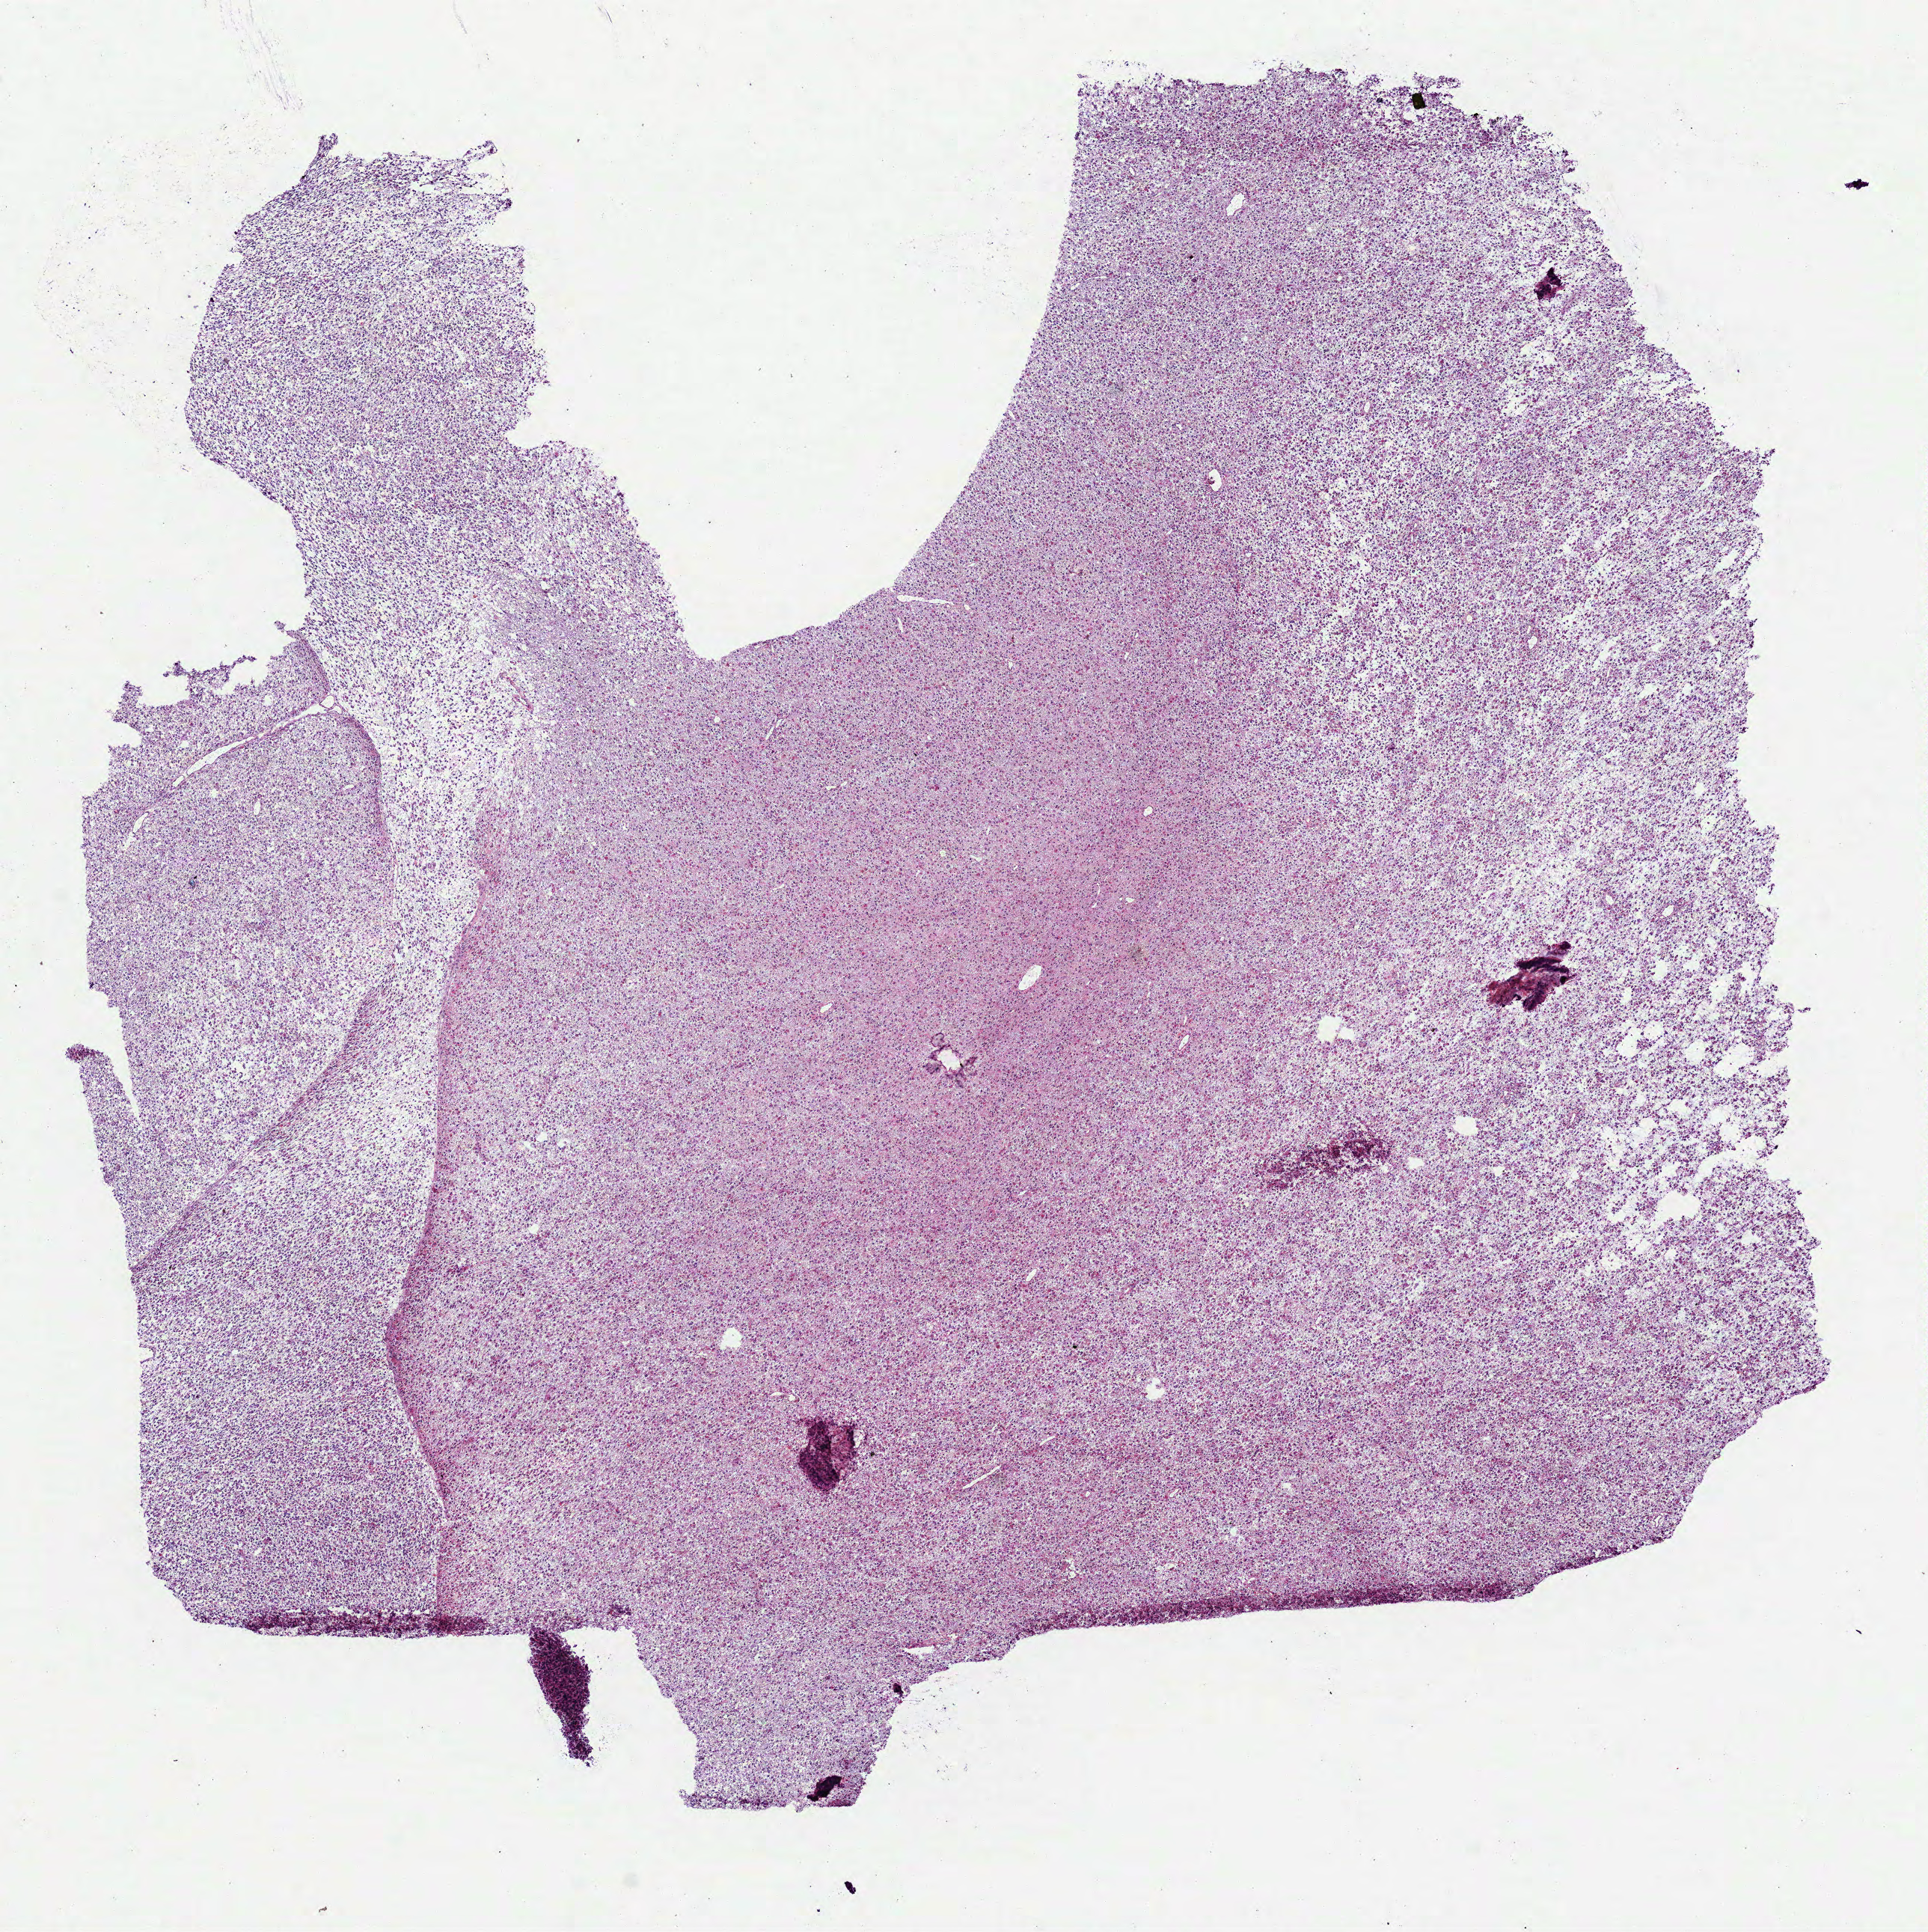
Whole-slide histology image, H&E-stained, low-resolution overview of the scanned area, about 10.4 x 10.4 mm; frozen section from the bottom of the tissue portion; primary tumour sample from the brain. Male, age 25 years at initial diagnosis. Histologic grade: G3 (poorly differentiated). Slide review estimates, as recorded: tumour cells 100%, tumour nuclei 80%, normal cells 0%, stromal cells 0%, necrosis 0%.
Laterality: right. Pathologic diagnosis: Mixed glioma.